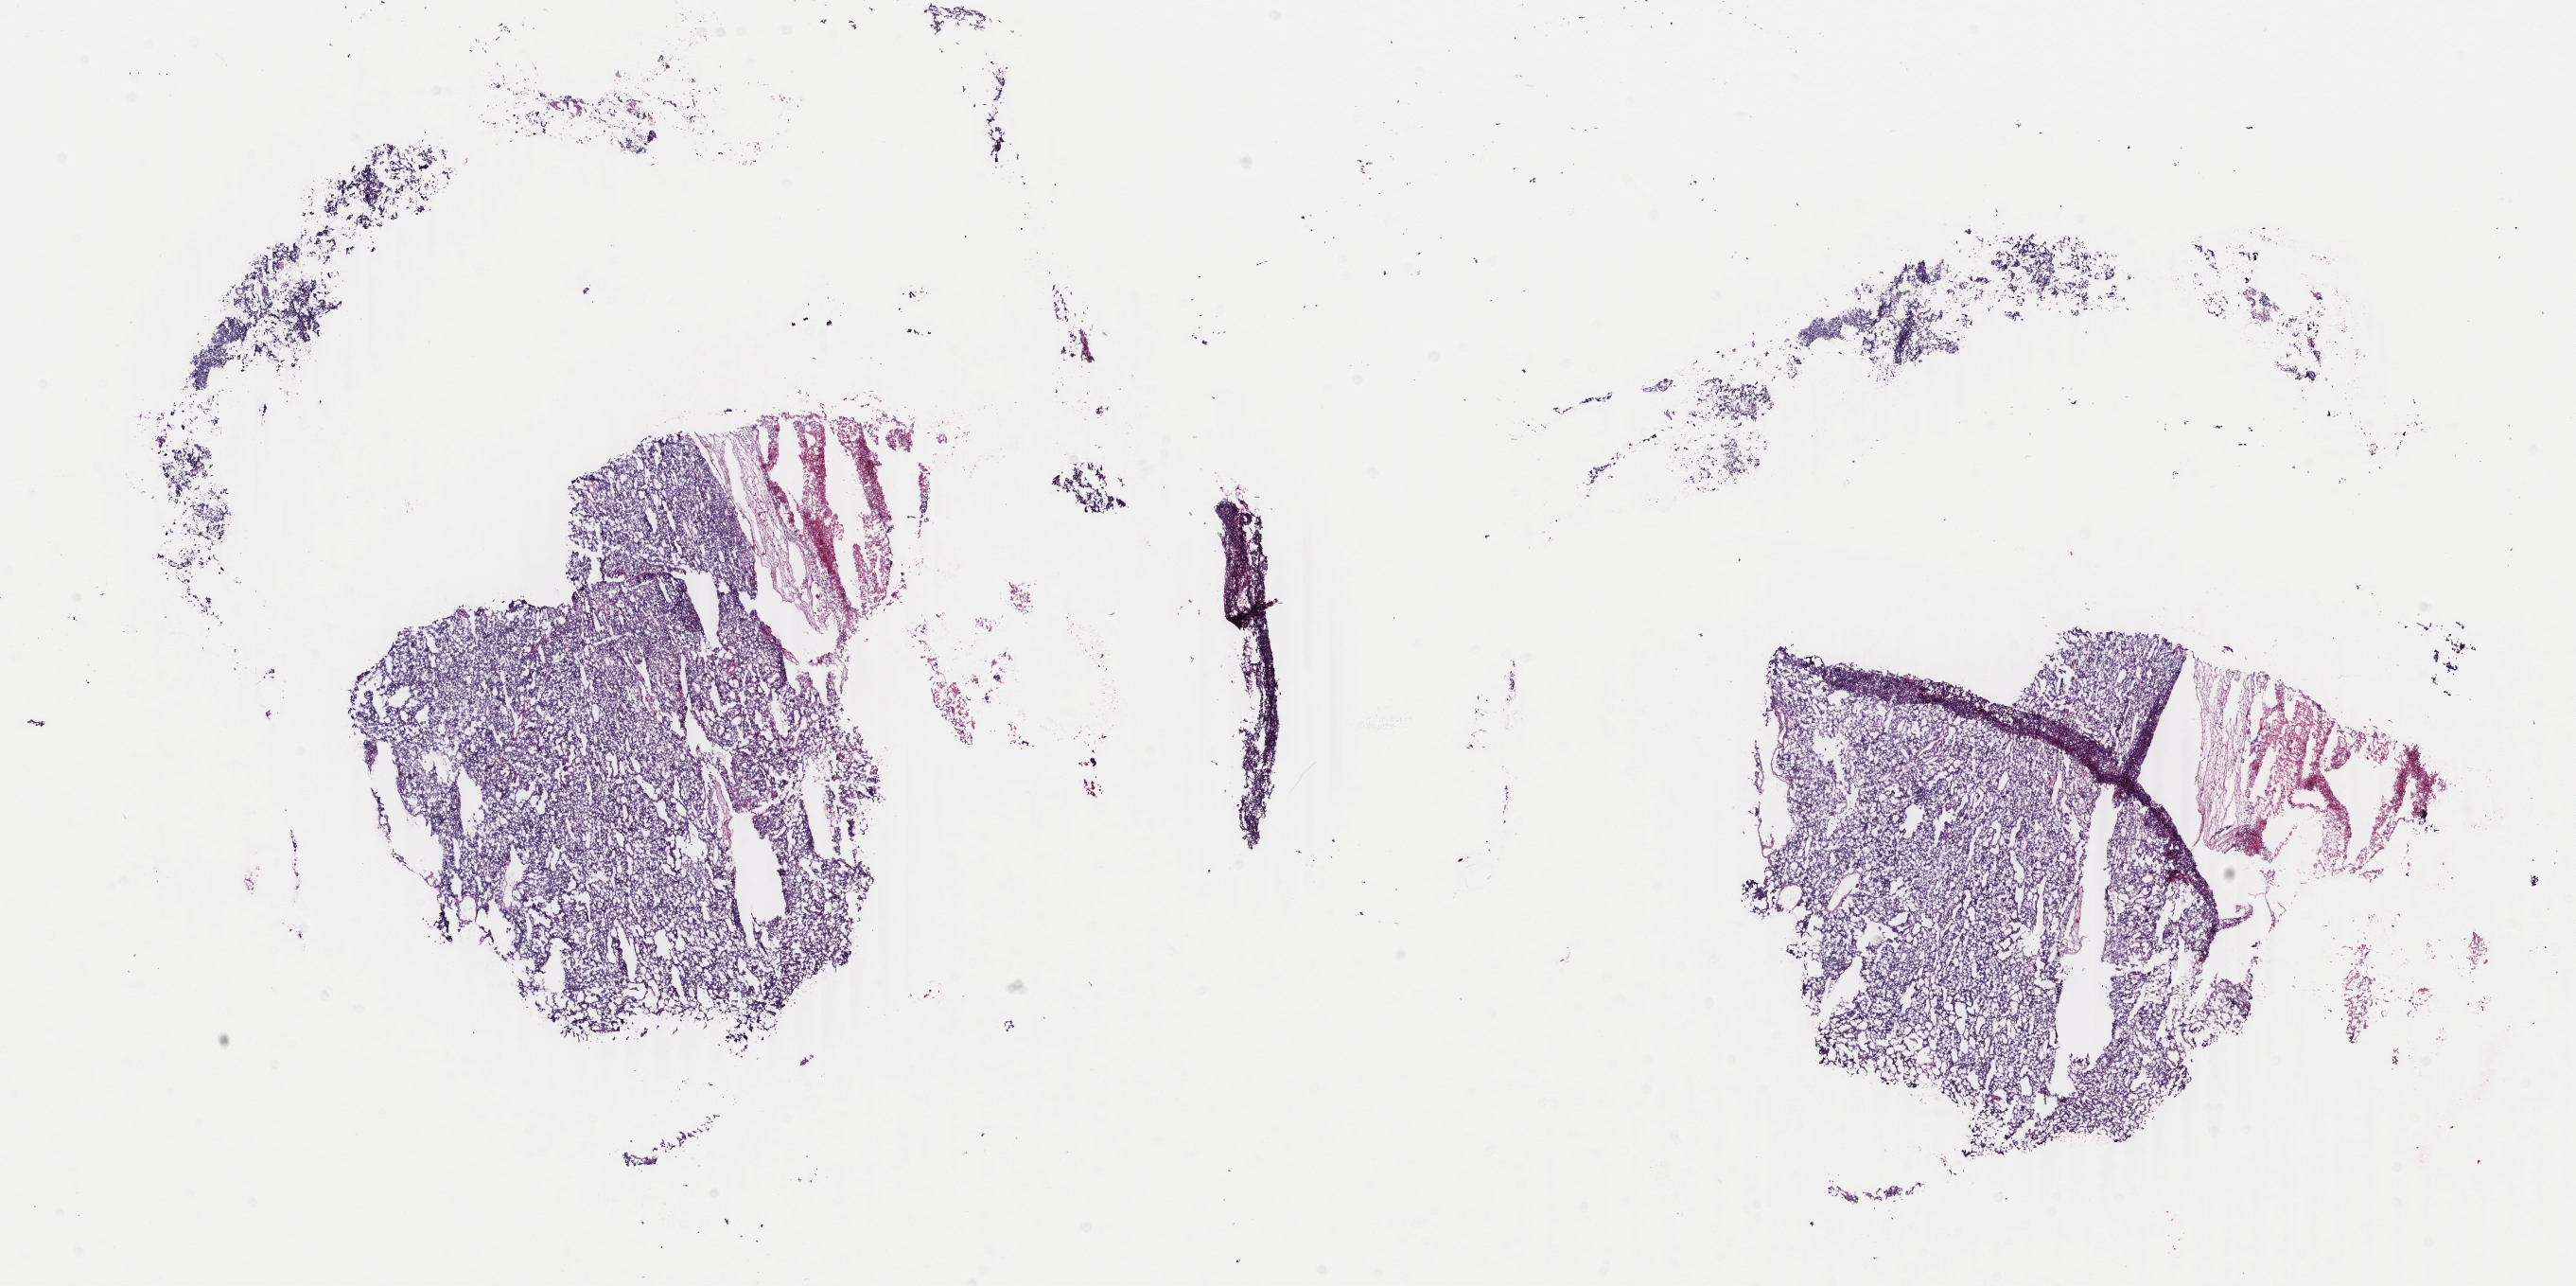
H&E whole-slide image, shown as a low-resolution overview of the whole scanned area (about 21.7 x 10.8 mm, slide scanned at 40x); frozen section; uterus, primary tumour sample. Female patient; age at initial diagnosis 59 years. Histologic grade: G3 (poorly differentiated). Pathologist review of this section (percent, as recorded): tumour cells 80%, tumour nuclei 80%, normal cells 0%, stromal cells 5%, necrosis 15%. Infiltration values recorded for this section: lymphocyte infiltration 2%, monocyte infiltration 0%, neutrophil infiltration 1%.
Lymph nodes positive (case pathology): 0 of 34 examined. FIGO stage: IIA. Diagnosis: Endometrioid adenocarcinoma, NOS (endometrium).